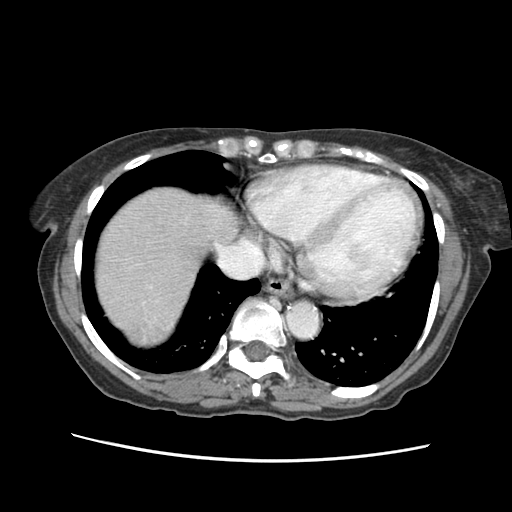
Contrast-enhanced abdominal CT (liver protocol), one axial slice; position 54 of 63 along the scan axis; 120 kVp; soft-tissue window (W 400 / L 40 HU); 512 × 512 image matrix. Case-level facts recorded for this patient, not image findings: diagnosis: hepatocellular carcinoma (patient treated with transarterial chemoembolisation; whether this scan precedes or follows treatment is not stated here); TNM stage (as recorded): Stage-I; Child-Pugh class: B; tumour differentiation: well differentiated; tumour nodularity: uninodular.
Structures marked on this image (semi-automatic segmentation, software-assisted and operator-edited):
- liver parenchyma outside the tumour (the mass and vessels are separate outlines, so this box may not span the whole liver): bounding box (x1, y1, x2, y2) in pixels: (96, 186, 234, 342)
- mass: (129, 311, 166, 341)